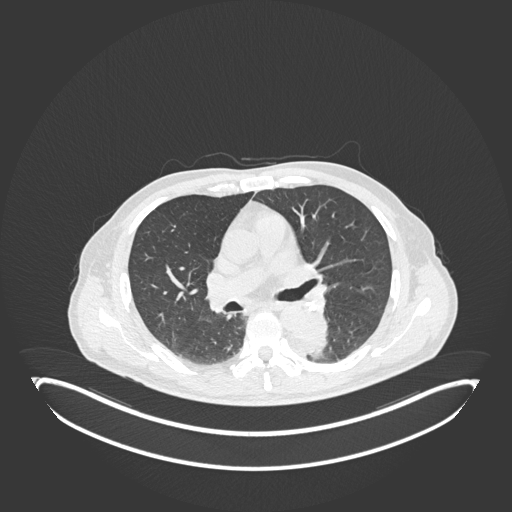
Chest CT, one axial slice. Slice 119 of 251 in the series (ordered by position). Reconstruction kernel B30f. 120 kVp. Lung window (W 1500 / L -600 HU). 512 × 512 image matrix. Male patient, age 72 years. Case-level facts recorded for this patient, not image findings: clinical TNM (as recorded): T2b N0 M1.
Structures marked on this image (bounding box drawn by a radiologist):
- lung tumour (recorded histology: adenocarcinoma): bounding box (x1, y1, x2, y2) in pixels: (297, 315, 330, 359)